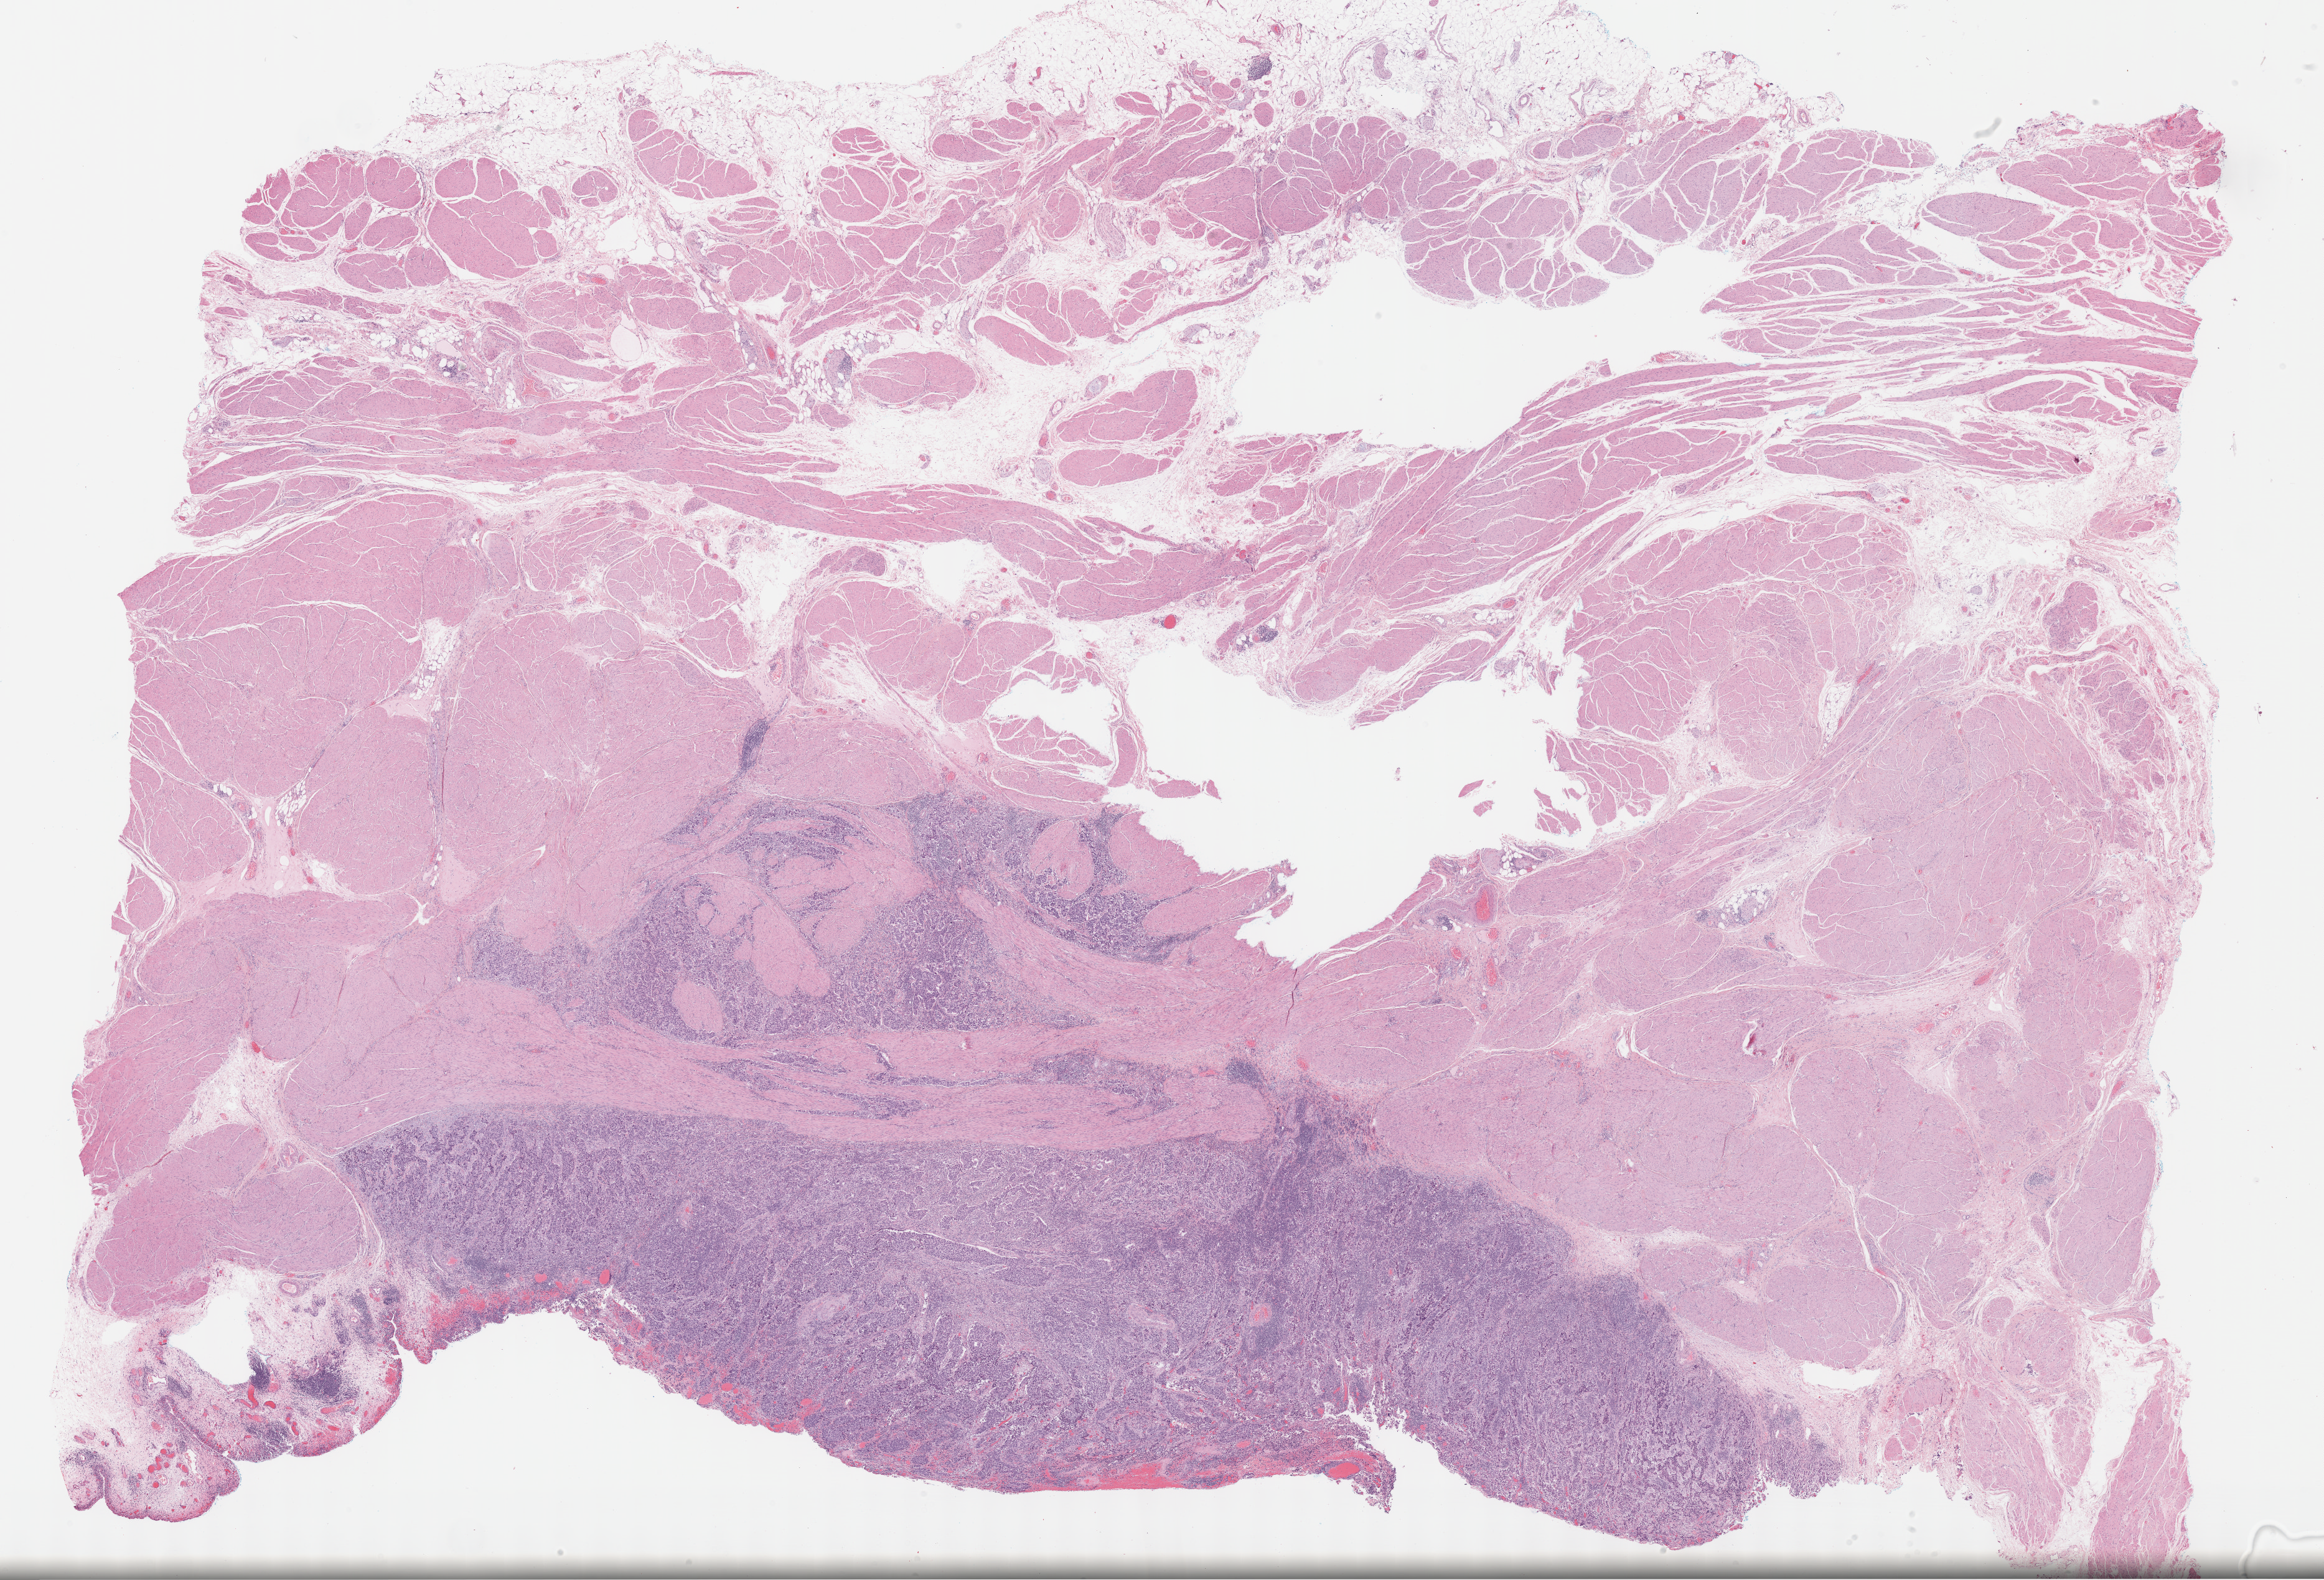
Digitized H&E tissue section (whole slide) — low-resolution overview of the scanned area, about 30.2 x 20.5 mm. Formalin-fixed paraffin-embedded (FFPE) diagnostic section. Sample: primary tumour, bladder. Patient: male, age at initial diagnosis 65 years. Histologic grade: high grade.
AJCC pathologic stage: IV (7th edition). TNM: T2b N2 M0. Pathologic diagnosis: Transitional cell carcinoma (posterior wall of bladder).